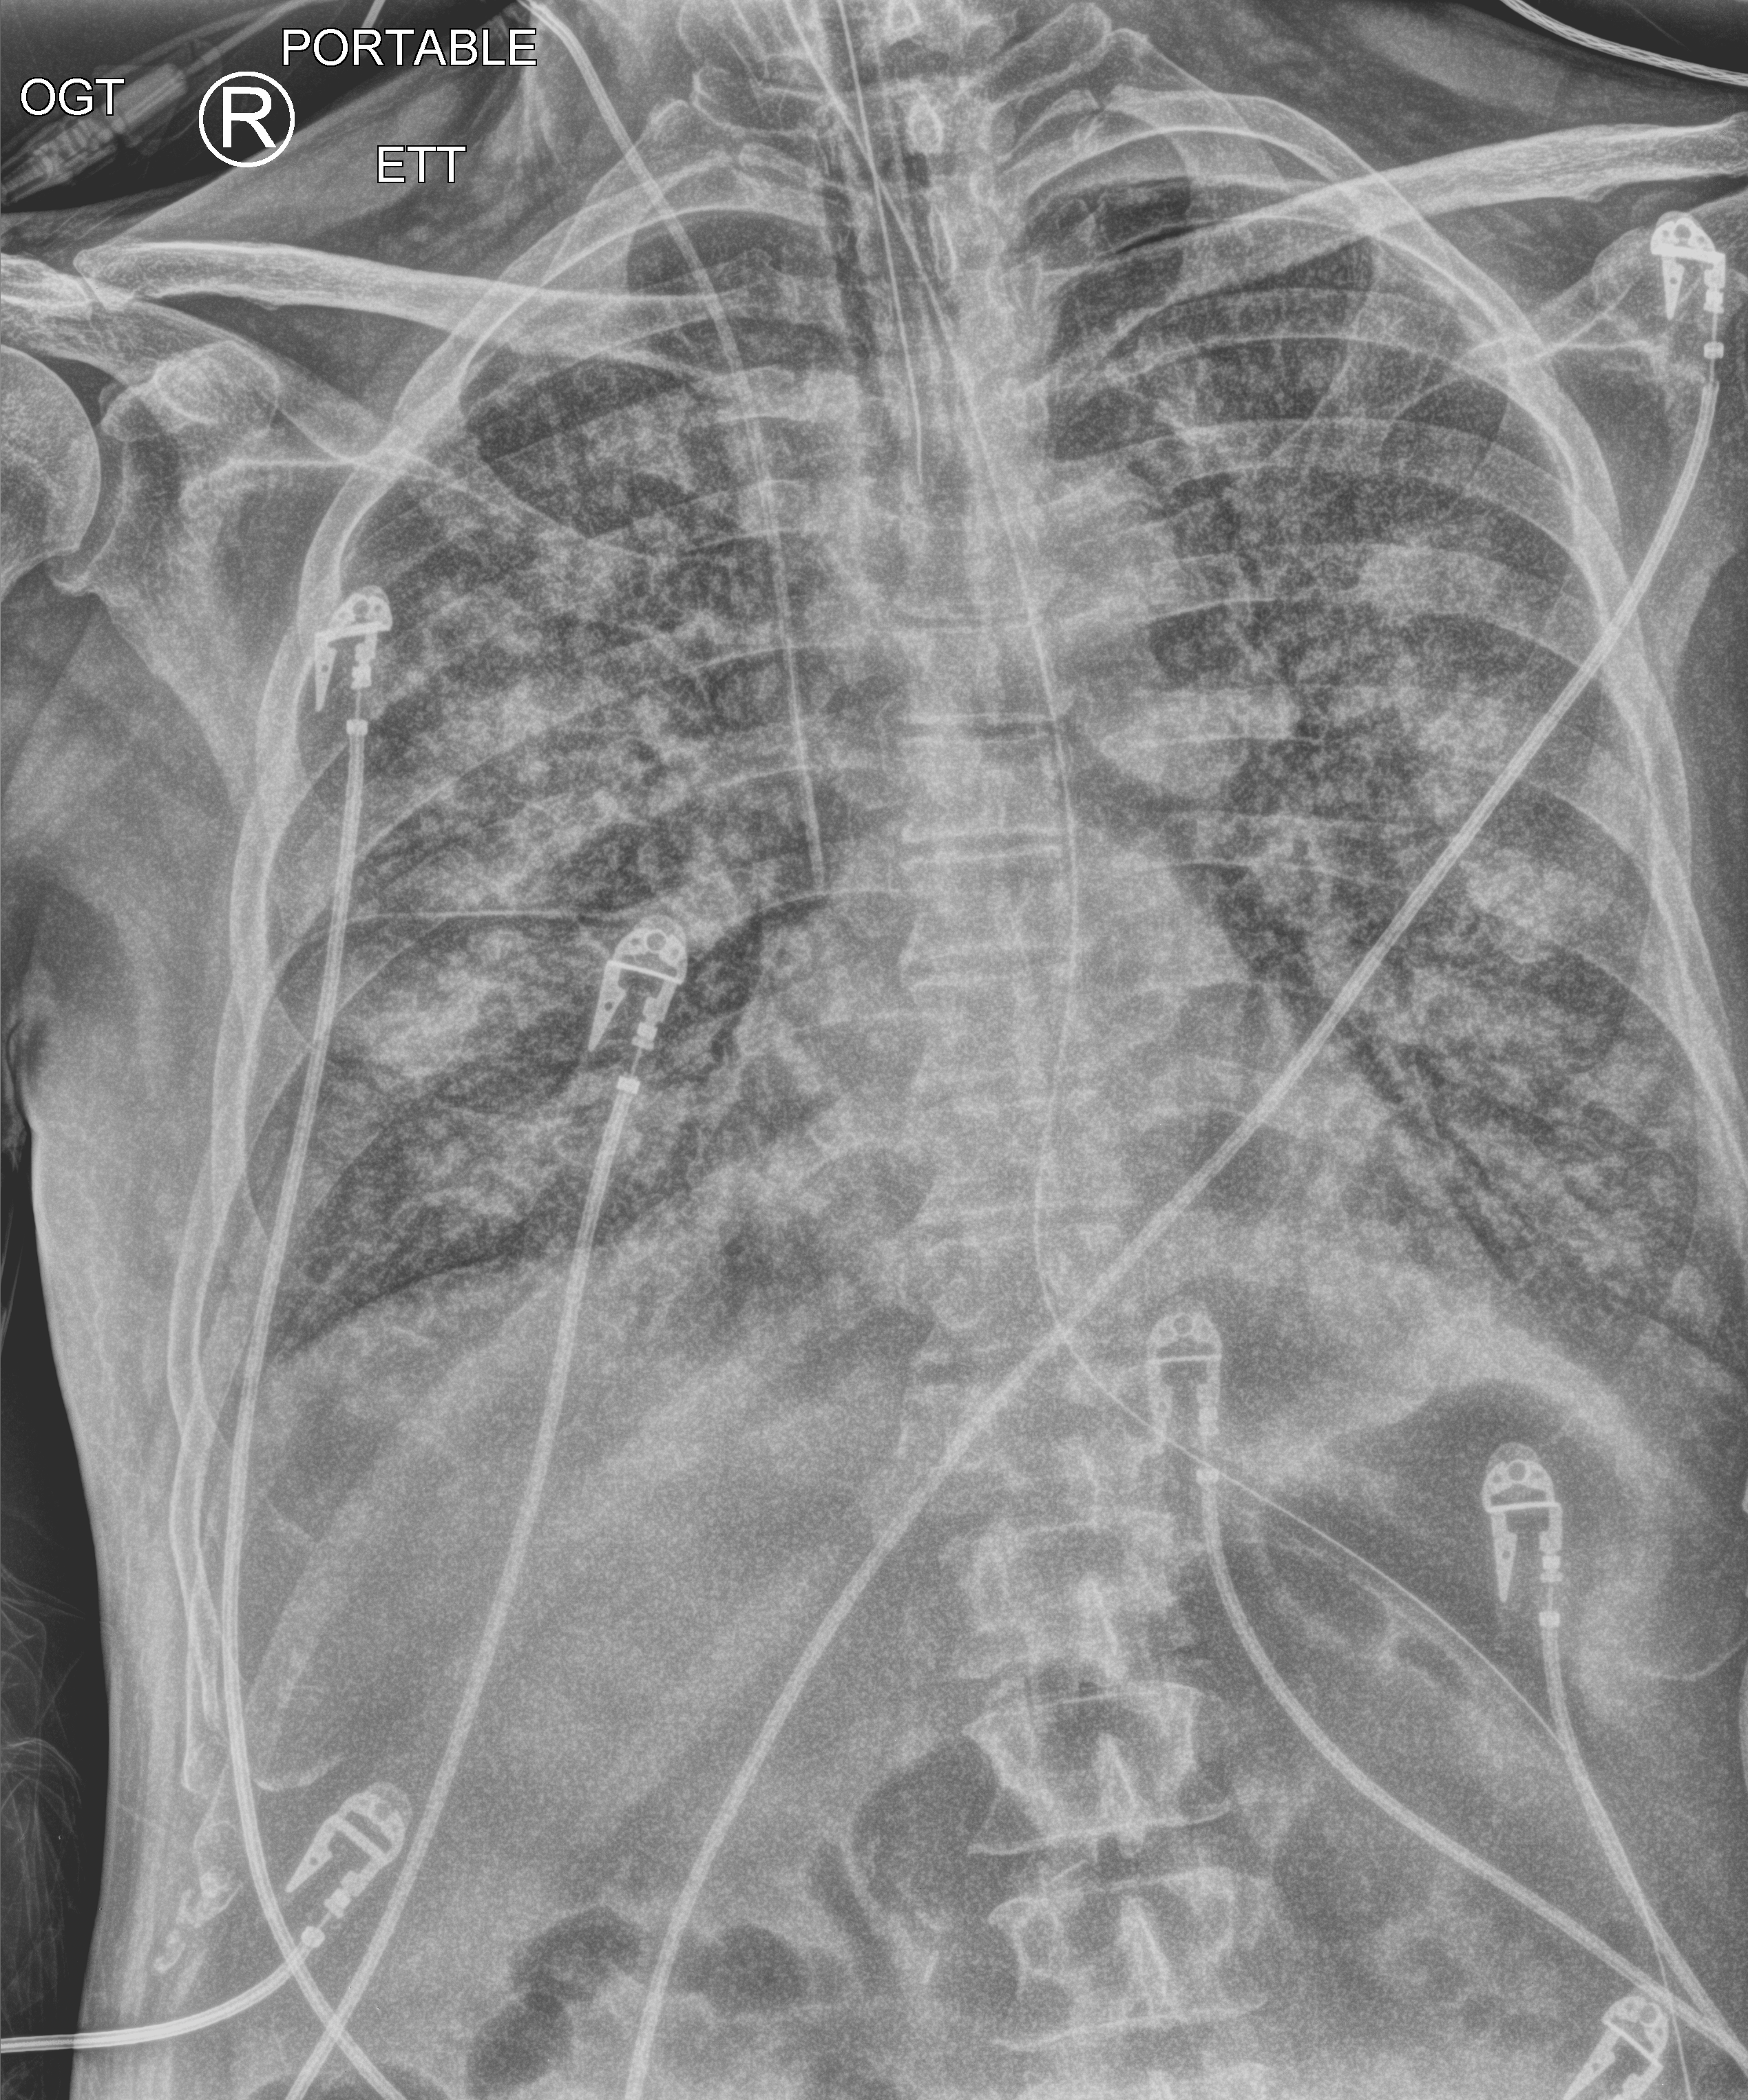
Portable chest radiograph, anteroposterior (AP) projection. Patient hospitalised with COVID-19; male, aged 60–74 years.
Admission-level facts for this patient (not findings on this image; timing relative to this image not recorded): mechanically ventilated during this hospital stay: yes.